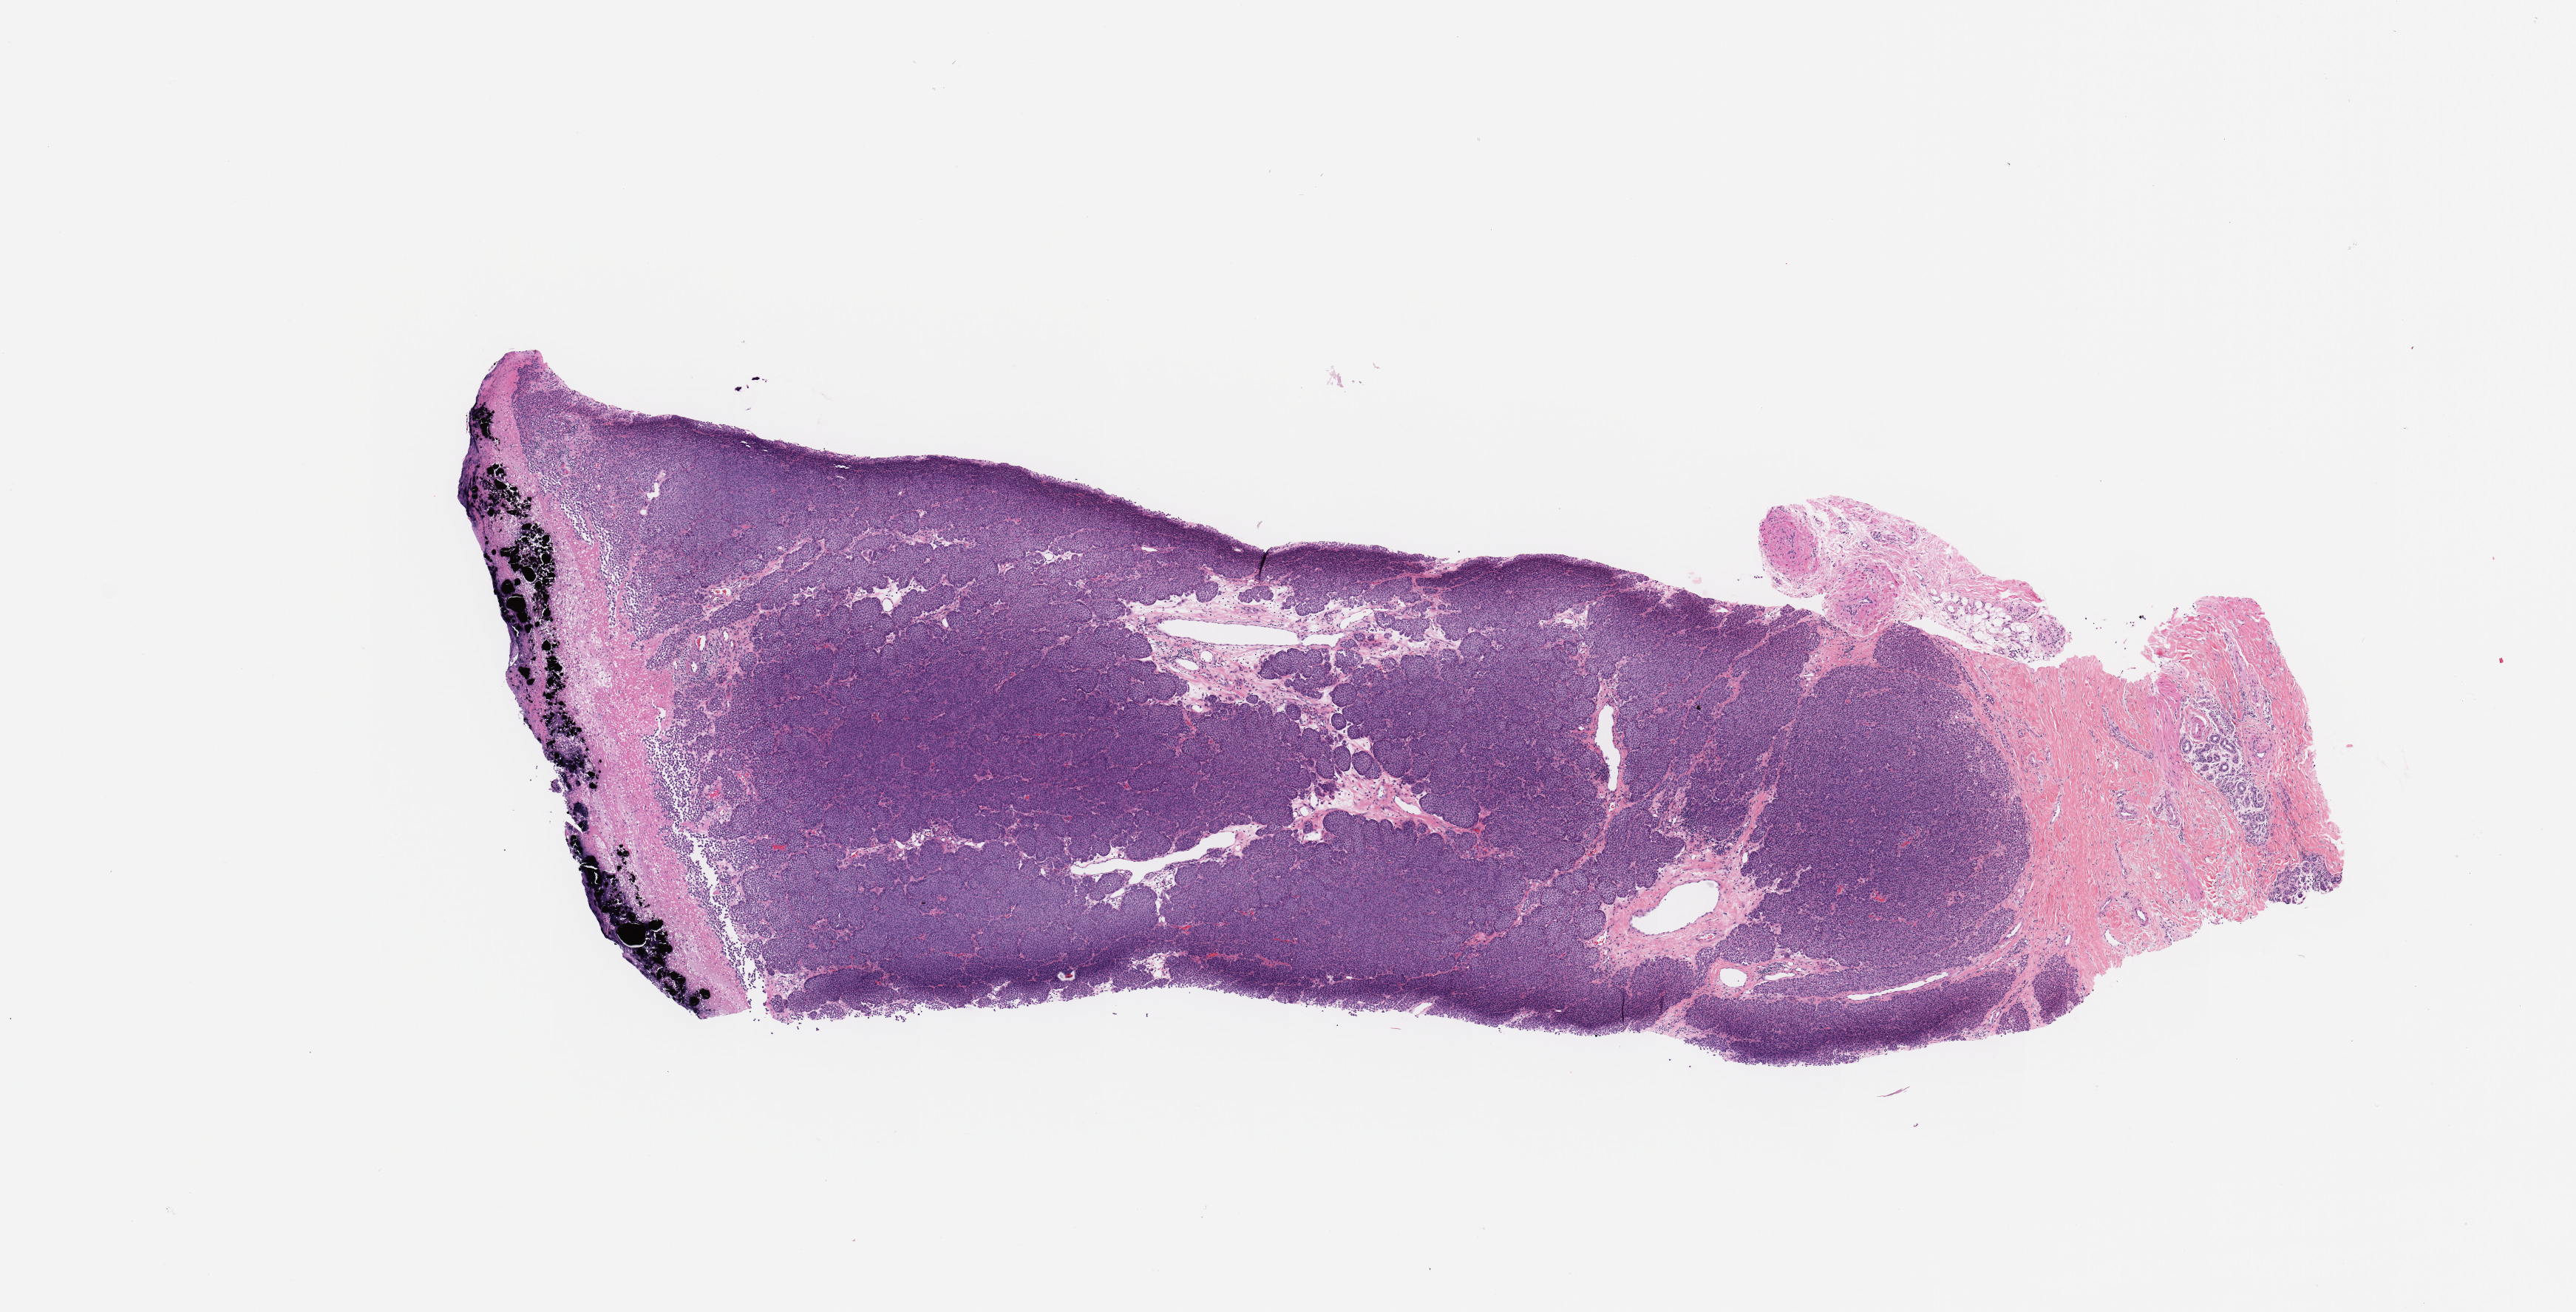
H&E-stained whole-slide image — a low-resolution overview of the entire scanned area, about 13.8 x 7.0 mm. Melanoma tumour tissue; sampled site not recorded. Male, 71 y/o.
• histologic diagnosis: Malignant melanoma, NOS
• AJCC pathologic stage: IIC
• primary tumour site (as recorded): extremities